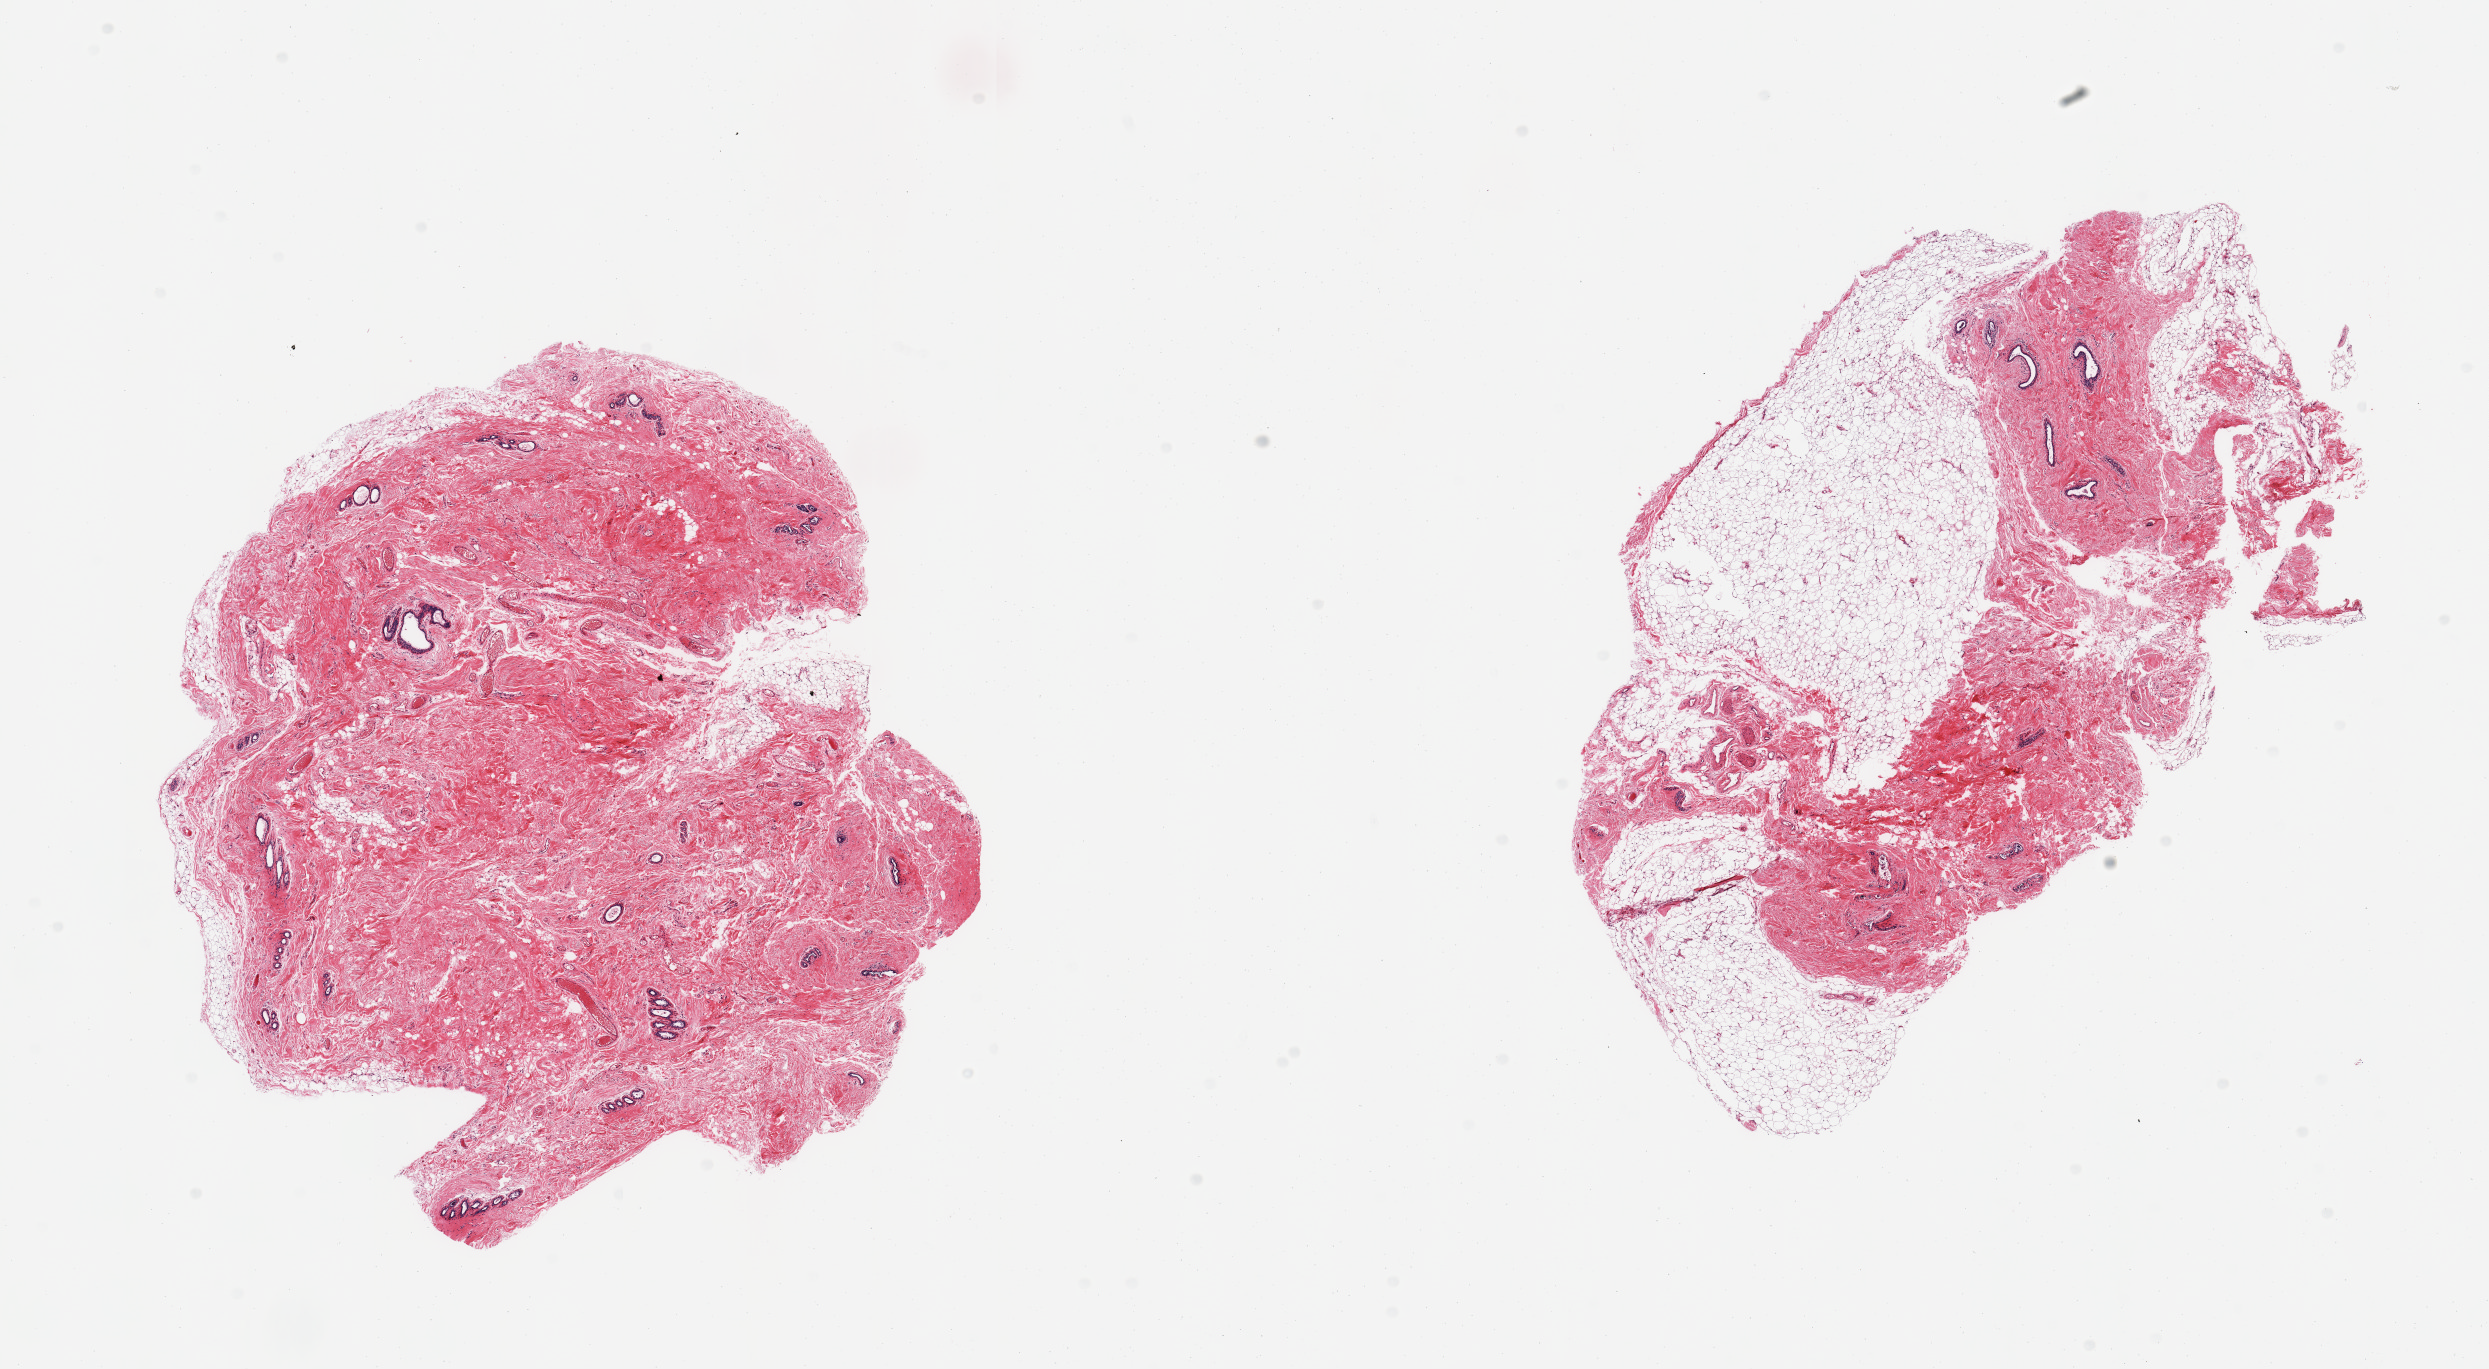
Digitized haematoxylin and eosin-stained section, low-resolution overview of the scanned area, about 19.7 x 10.8 mm. PAXgene-fixed paraffin-embedded (PFPE) section. Target tissue: breast. Donor tissue sample.
Reviewer comment on this tissue sample: 2 pieces; atrophic ducts in fibrofatty tiisue.